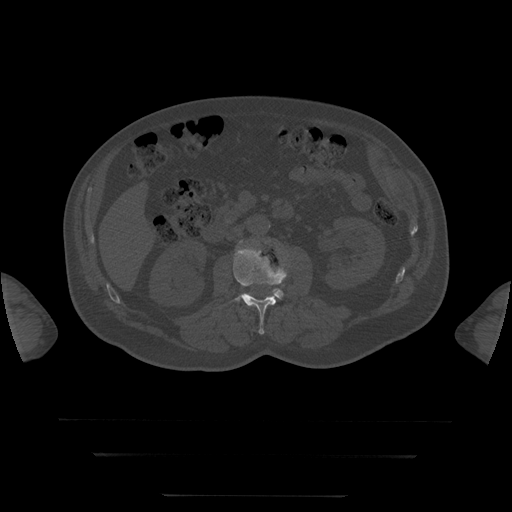
CT including the spine, one axial slice; slice 17 of 397 in the series (ordered by position); reconstruction kernel STANDARD; bone window (W 1800 / L 400 HU); 1.25 mm slice thickness; 512 × 512 image matrix, field of view 510 × 510 mm. Patient age 73 years. From the clinical record (not read from this slice): primary cancer: prostate.
Structures marked on this image (semi-automatically segmented with operator editing):
- L3 vertebra: box from (x=241, y=240) to (x=284, y=299) px